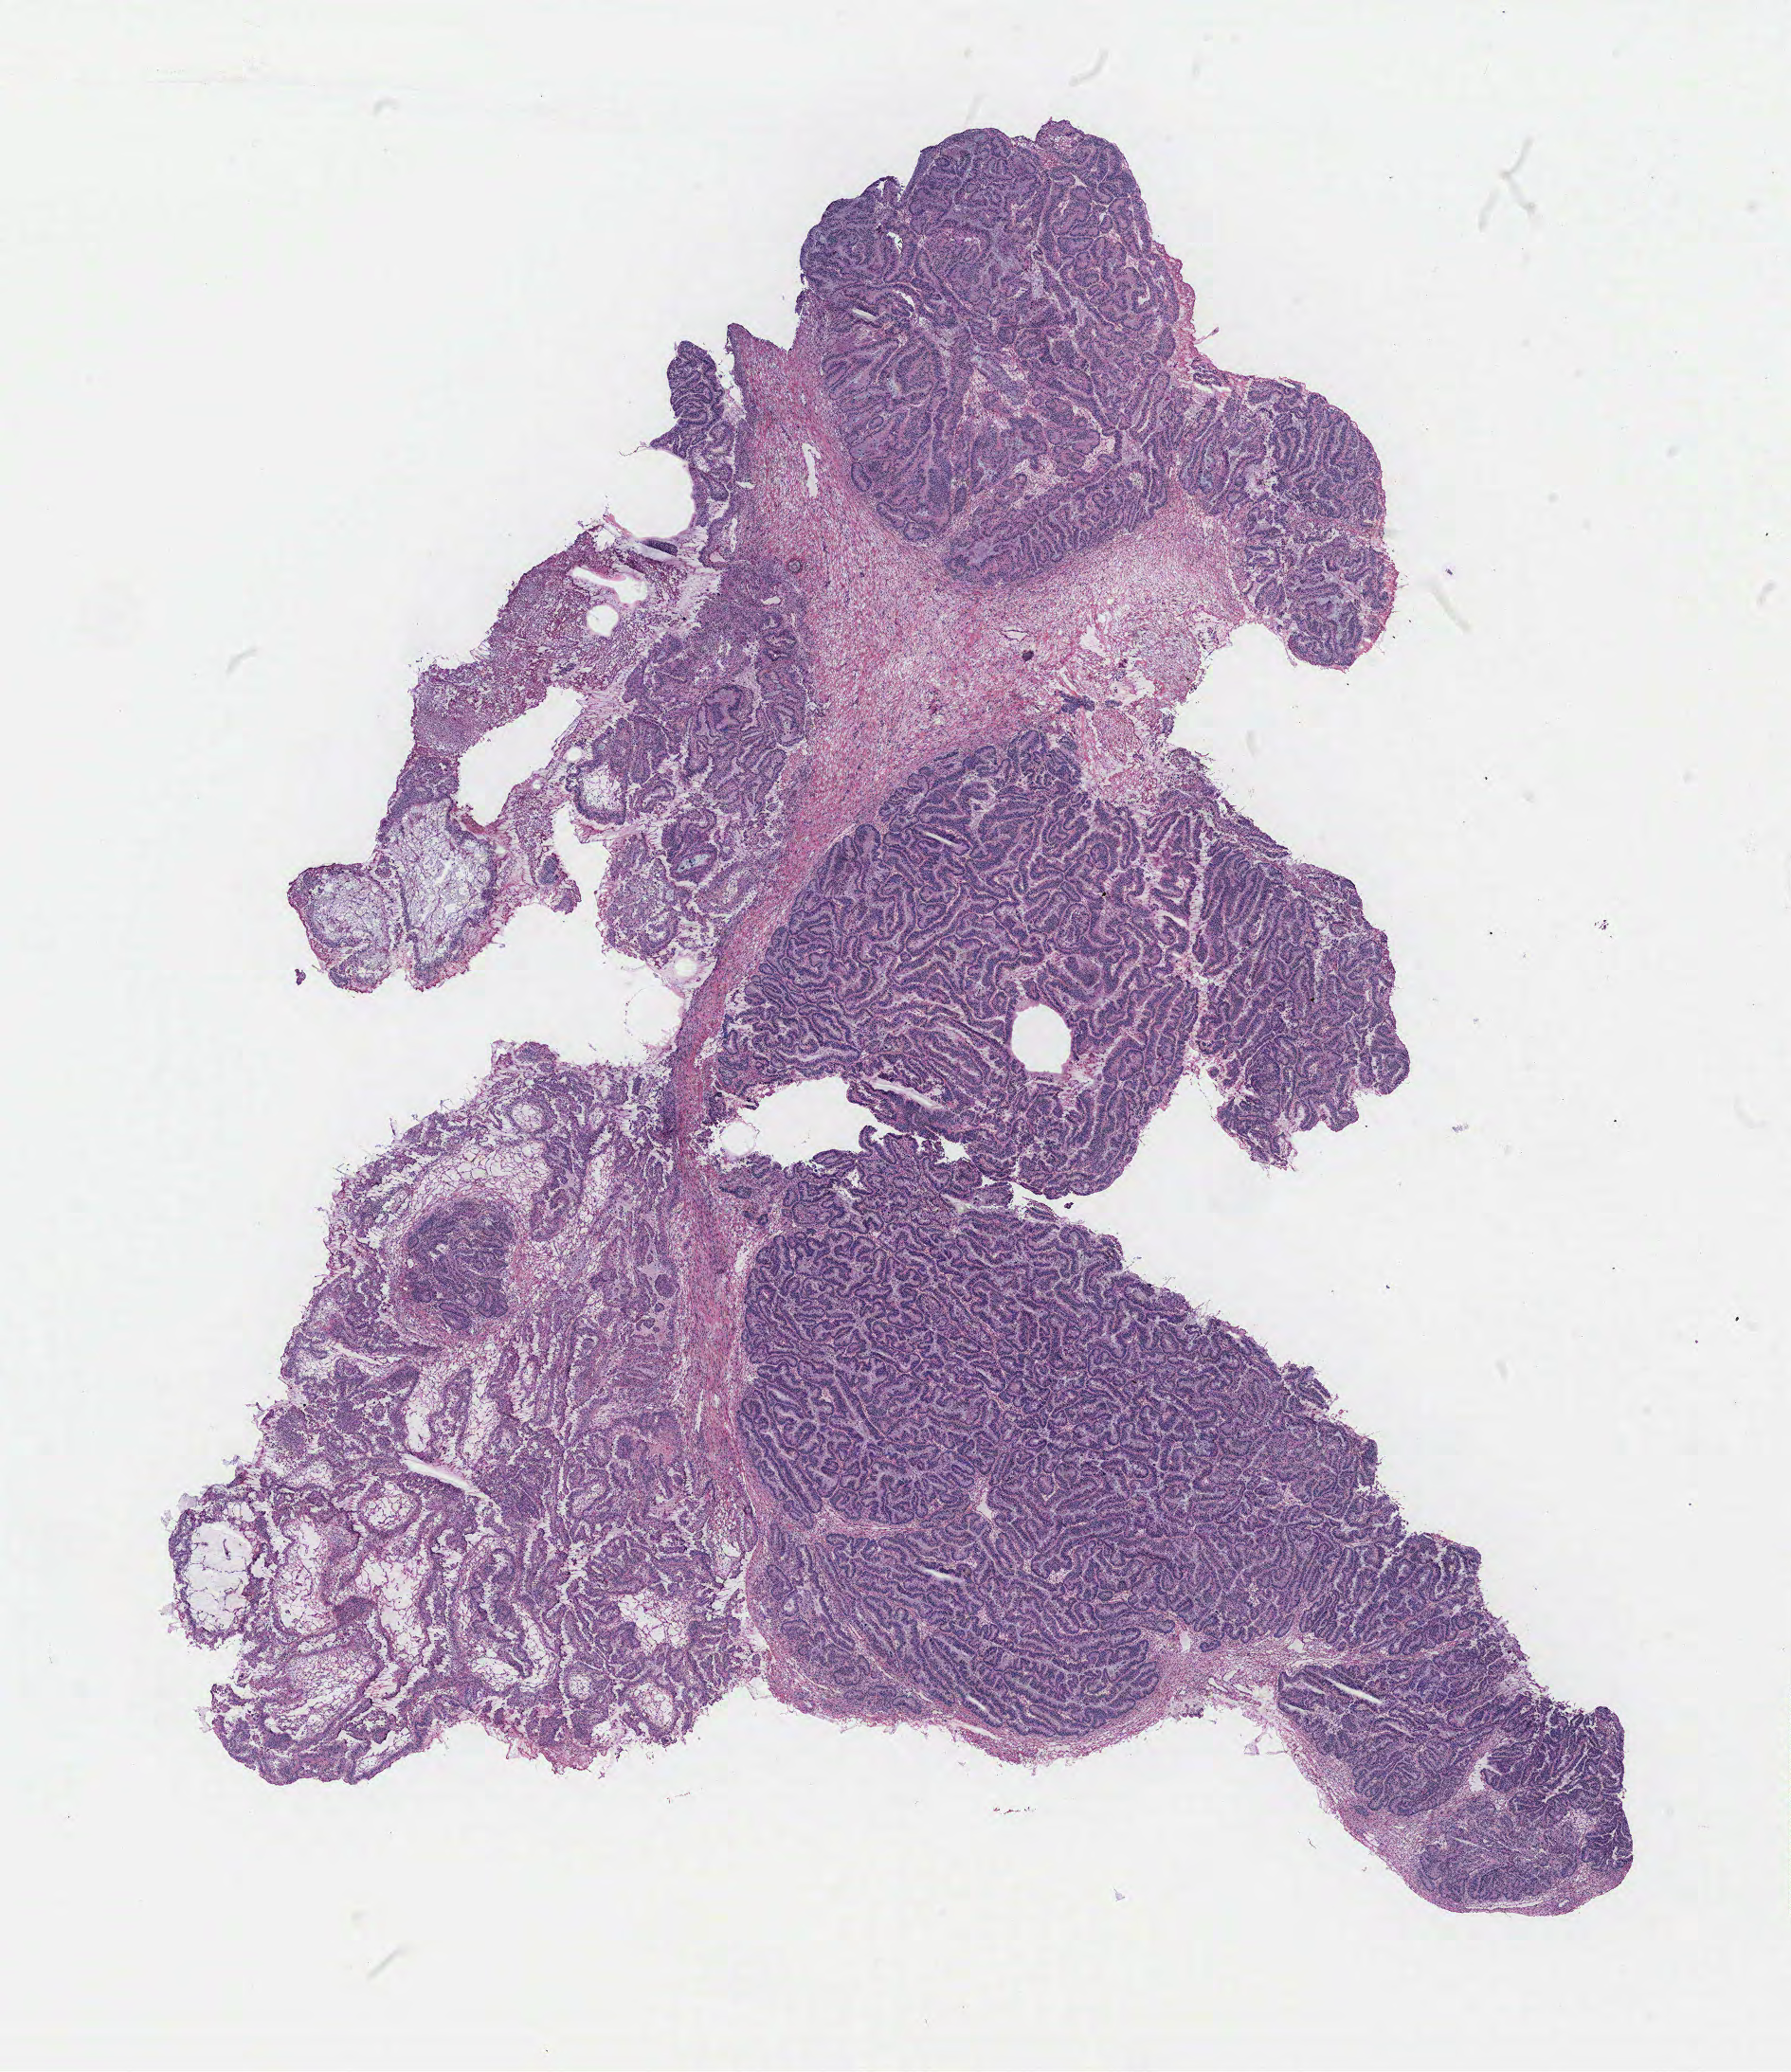
Whole-slide histology image, H&E — shown as a low-resolution overview of the whole scanned area (about 15.1 x 17.5 mm, slide scanned at 40x); ovary, tissue type not recorded. Female patient.
• patient diagnosis: Serous adenocarcinoma, NOS